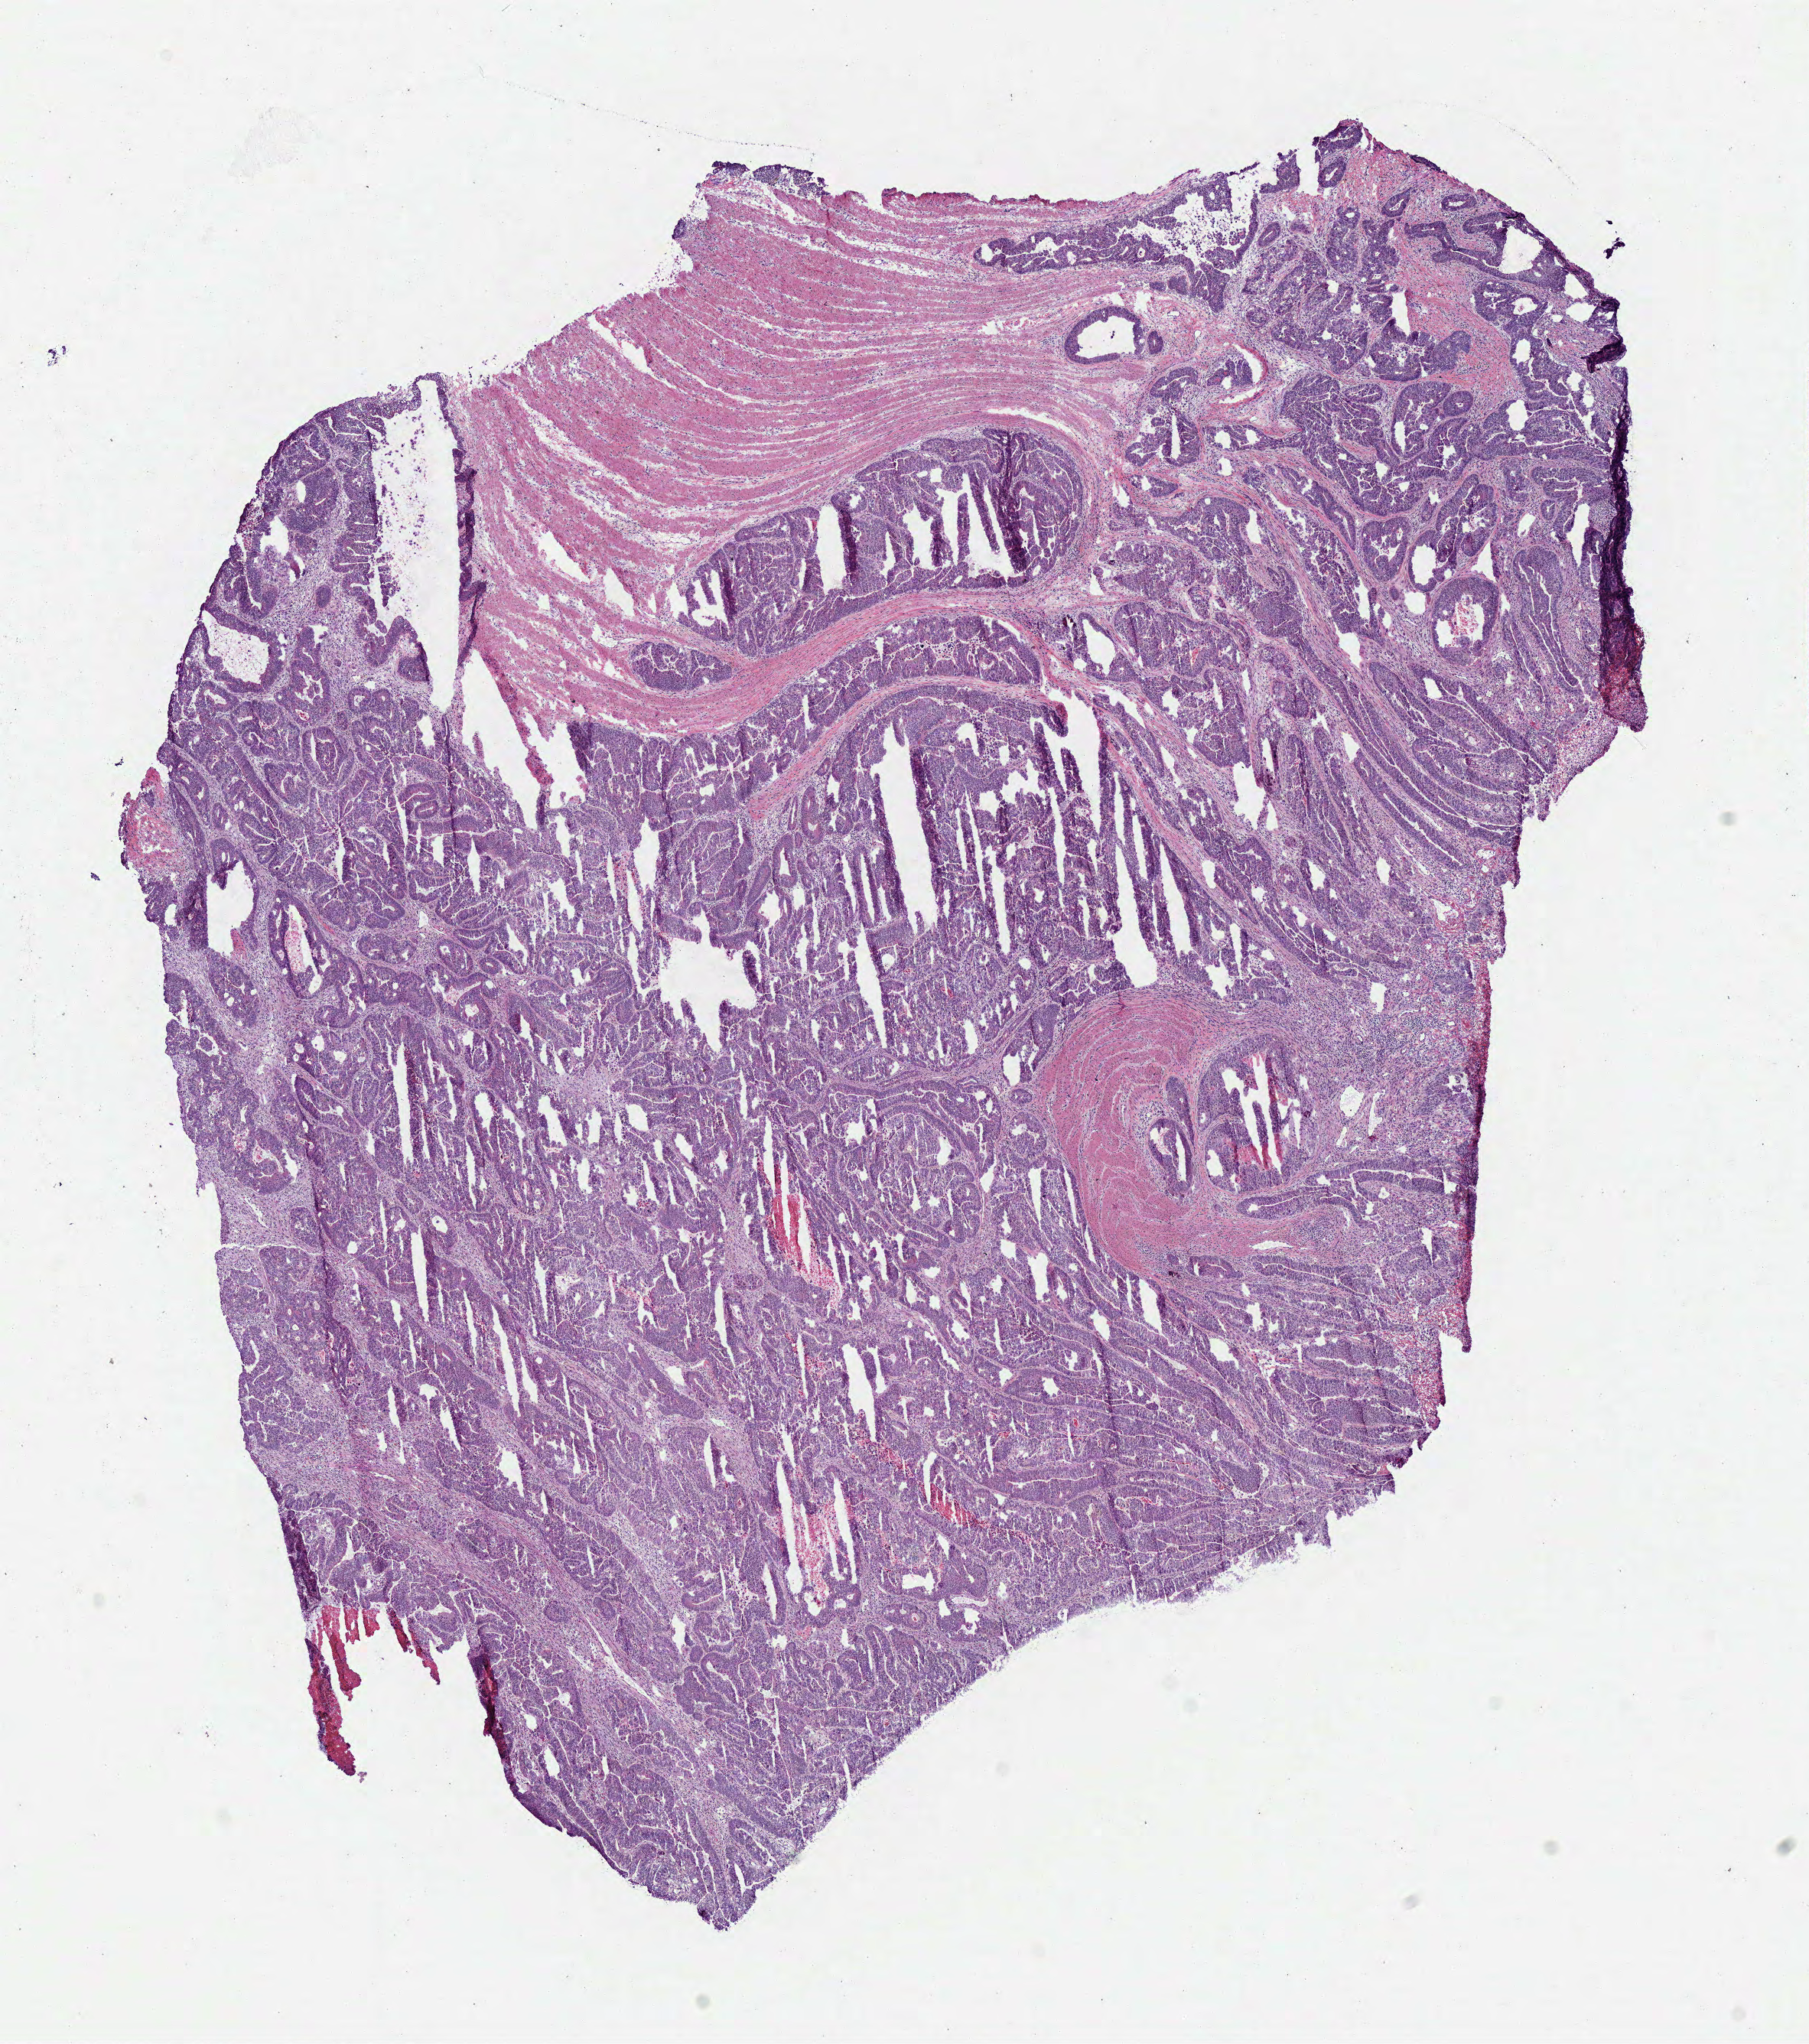
H&E whole-slide image, shown as a low-resolution overview of the whole scanned area (about 9.3 x 10.5 mm, acquisition: 40x scan), frozen section, primary tumour sample from the colon. Patient: female, age at initial diagnosis 54 years. Composition of this section per pathologist review: tumour cells 75%, tumour nuclei 80%, normal cells 0%, stromal cells 20%, necrosis 5%.
Diagnosis: Adenocarcinoma, NOS (sigmoid colon). Lymph nodes positive (case pathology): 1 of 25 examined. AJCC pathologic stage: IV (6th edition).